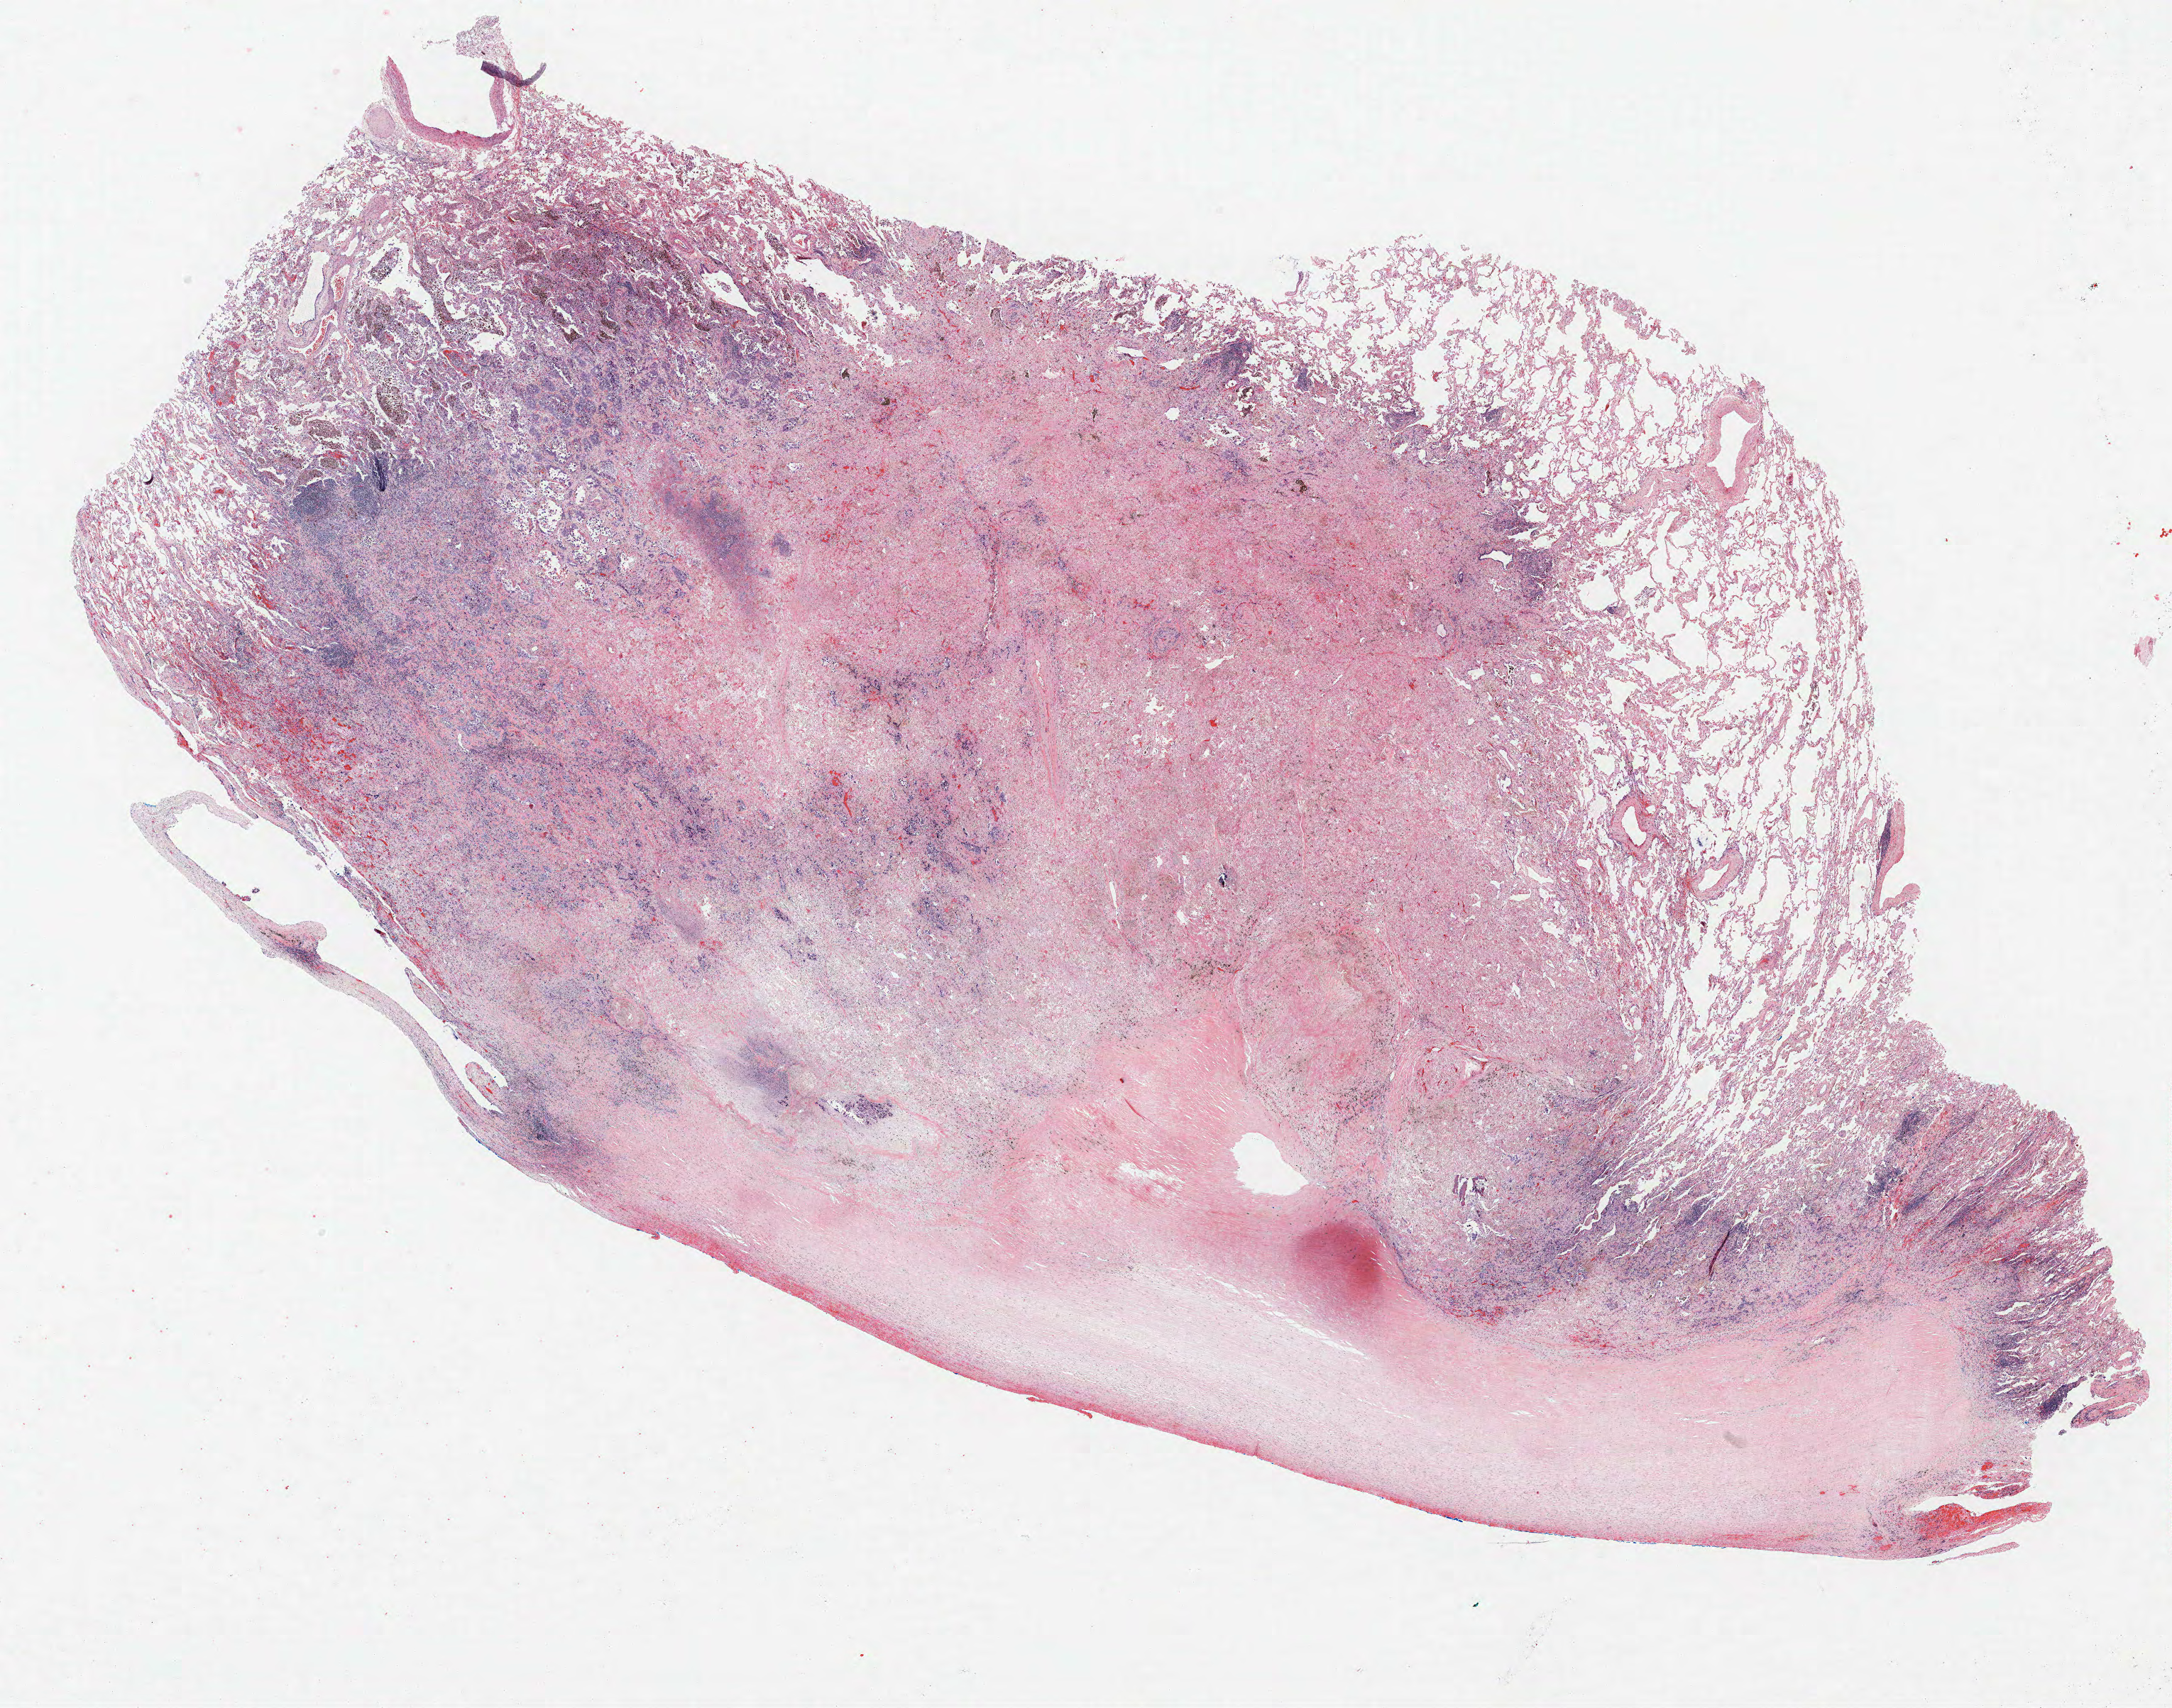
H&E whole-slide image, a low-resolution overview of the entire scanned area, about 24.5 x 19.3 mm, FFPE section, lung. Female, age 61 at enrolment. Current smoker at enrolment. Grade: poorly differentiated (G3).
• ICD-O-3 topography: upper lobe of lung (C34.1)
• tumour size (pathology): 17 mm
• stage (AJCC 6th edition): IB
• primary tumour location (clinical record): left upper lobe
• participant's lung-cancer diagnosis: Adenocarcinoma, NOS (ICD-O-3 8140/3)